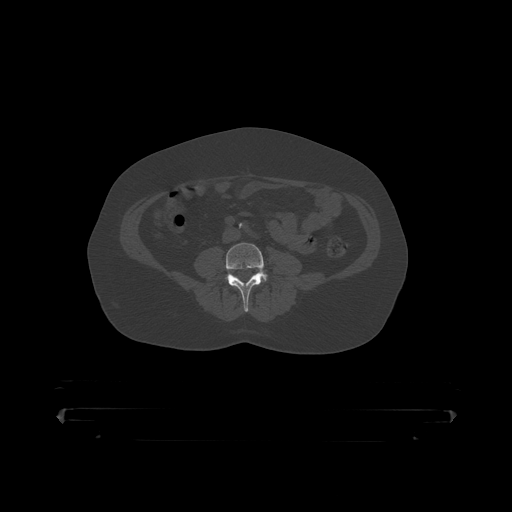
CT including the spine, one axial slice; slice 62 of 390 in the series (ordered by position); reconstruction kernel STANDARD; 120 kVp; bone window (W 1800 / L 400 HU); 1.25 mm slice thickness; 512 × 512 image matrix. Patient: male, 60 years. From the clinical record (not read from this slice): primary cancer: prostate.
Outlined on this slice (semi-automatic segmentation, software-assisted and operator-edited):
- L4 vertebra: bounding box <224,243,269,312> (left, top, right, bottom; pixels)